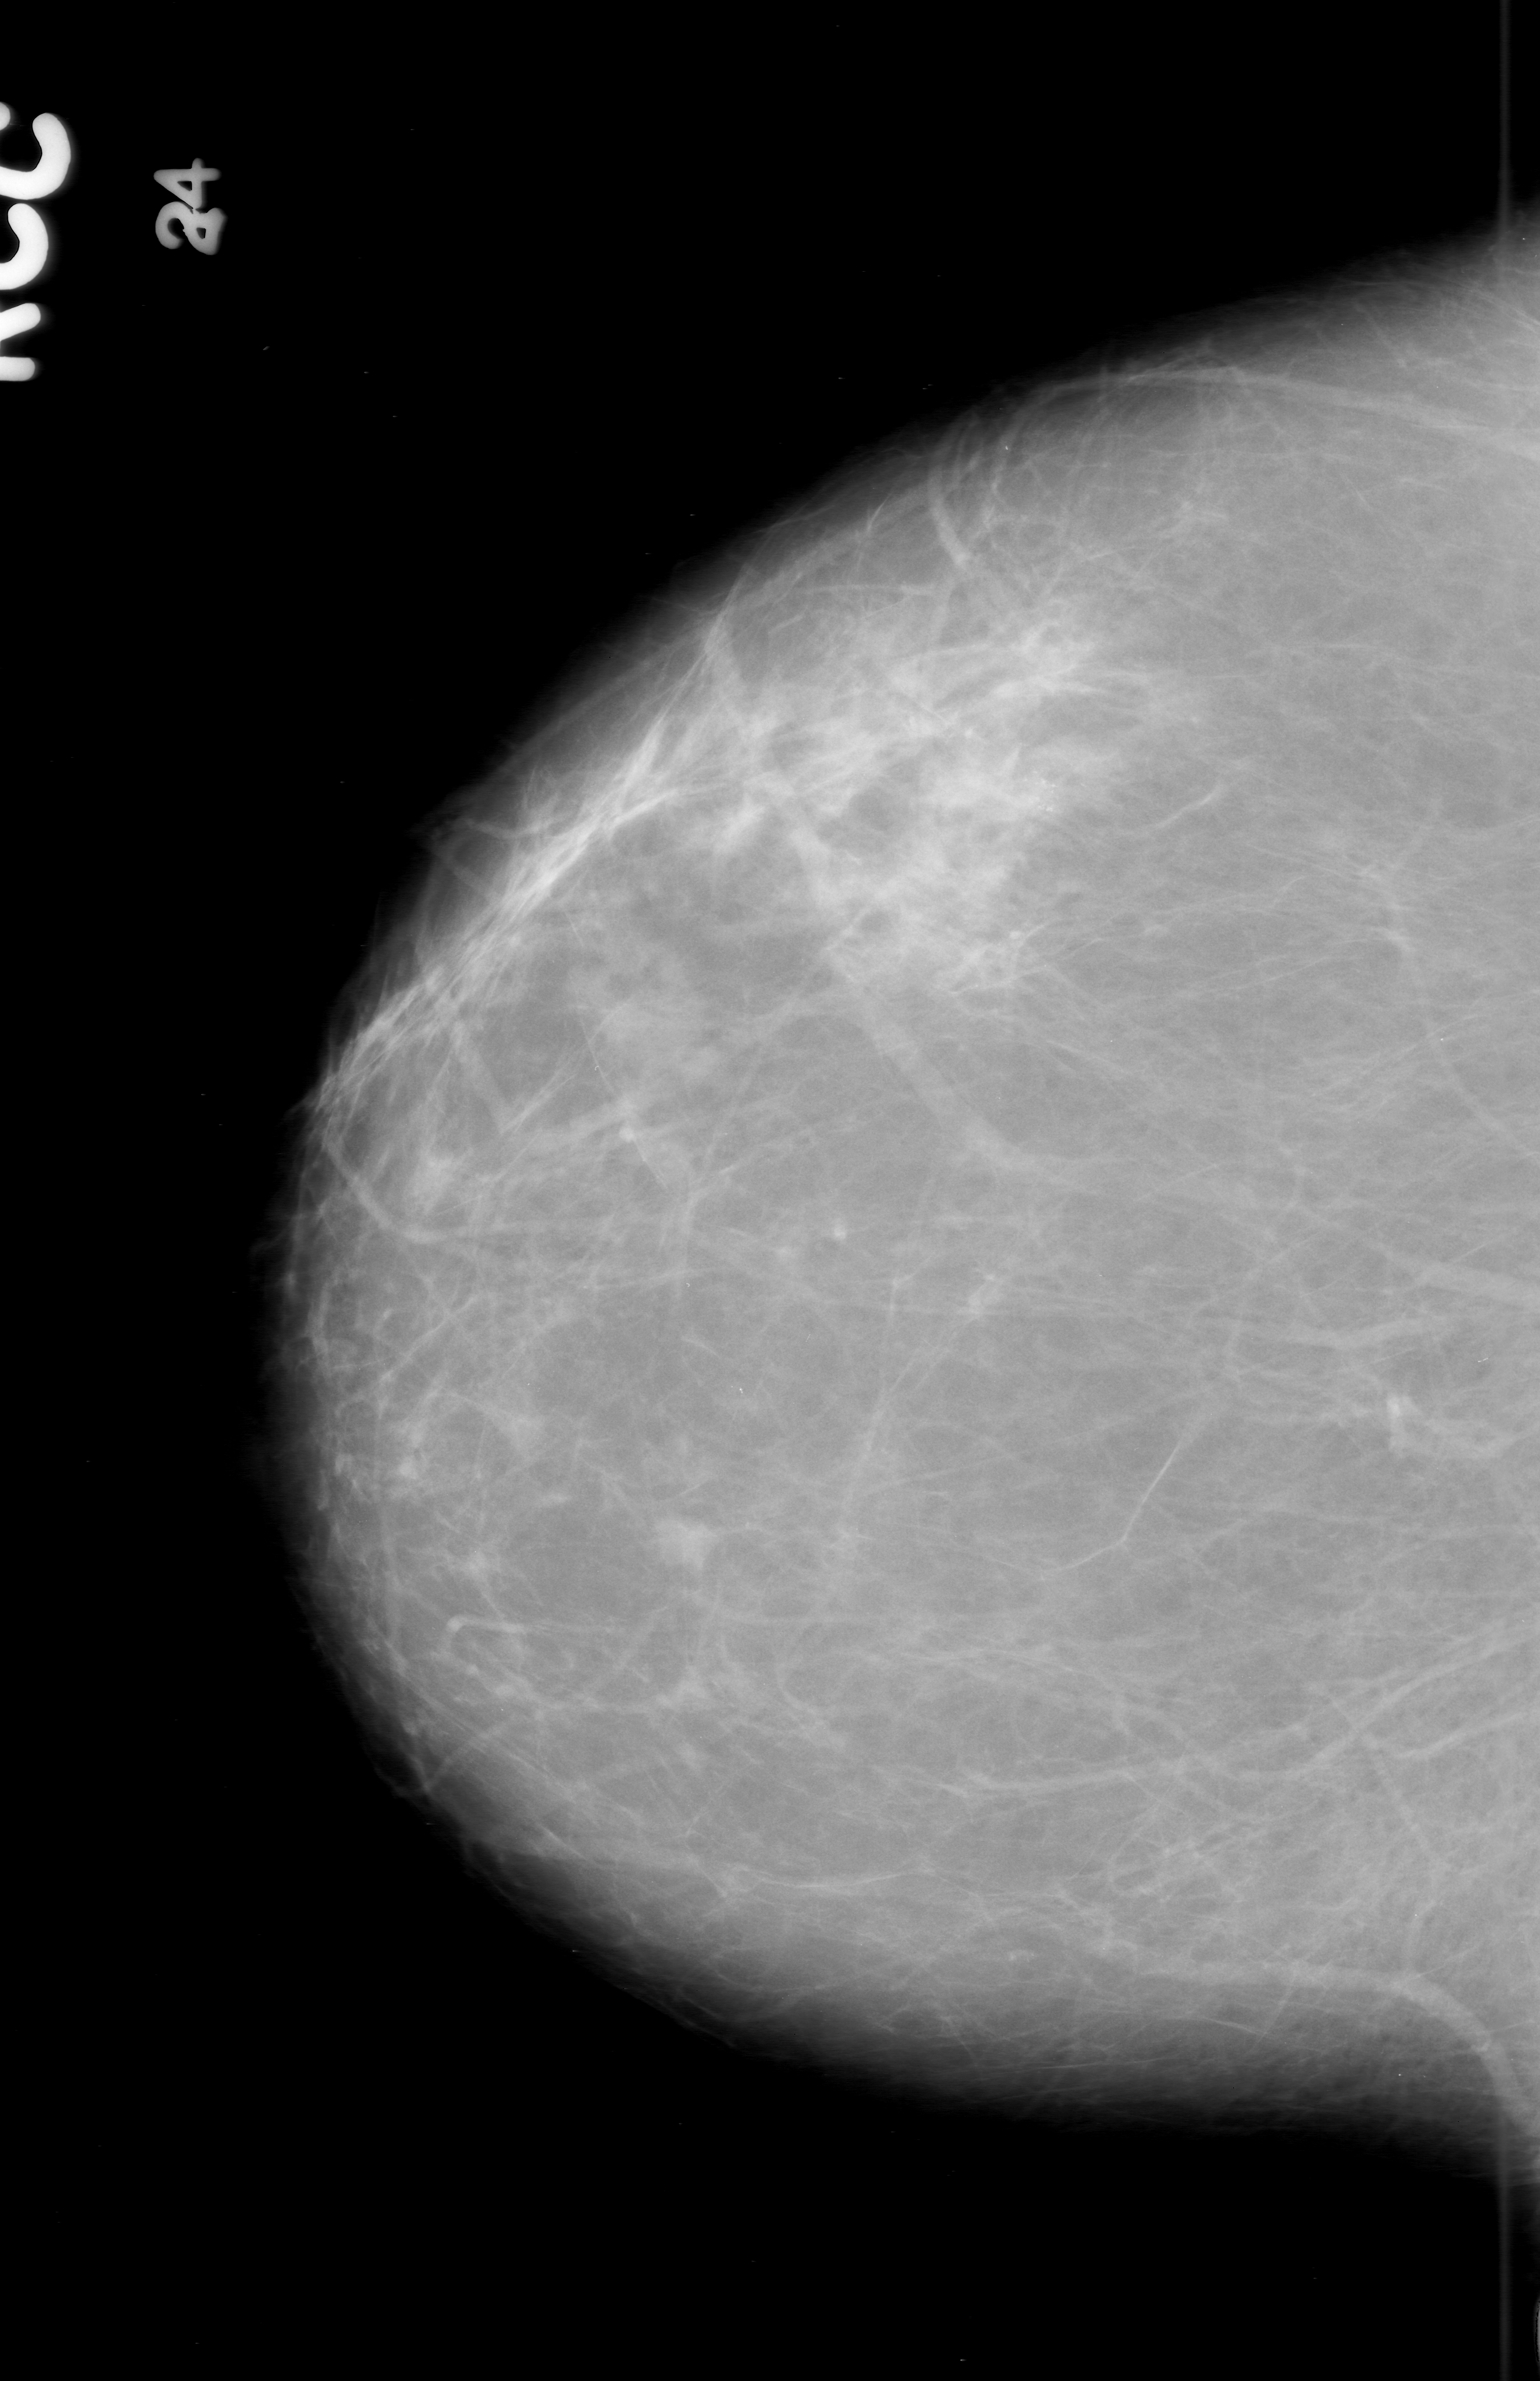
Digitized screen-film mammogram. Right breast. CC view. BI-RADS breast density category 2 (scale 1–4). 1540 × 2381 image matrix.
Expert-marked regions of interest on this image (one box per marked abnormality):
- calcifications, morphology pleomorphic, distribution clustered; BI-RADS assessment category 0 (incomplete: needs additional imaging); pathology (as recorded): benign: bounding box <917,707,1139,880> (left, top, right, bottom; pixels)